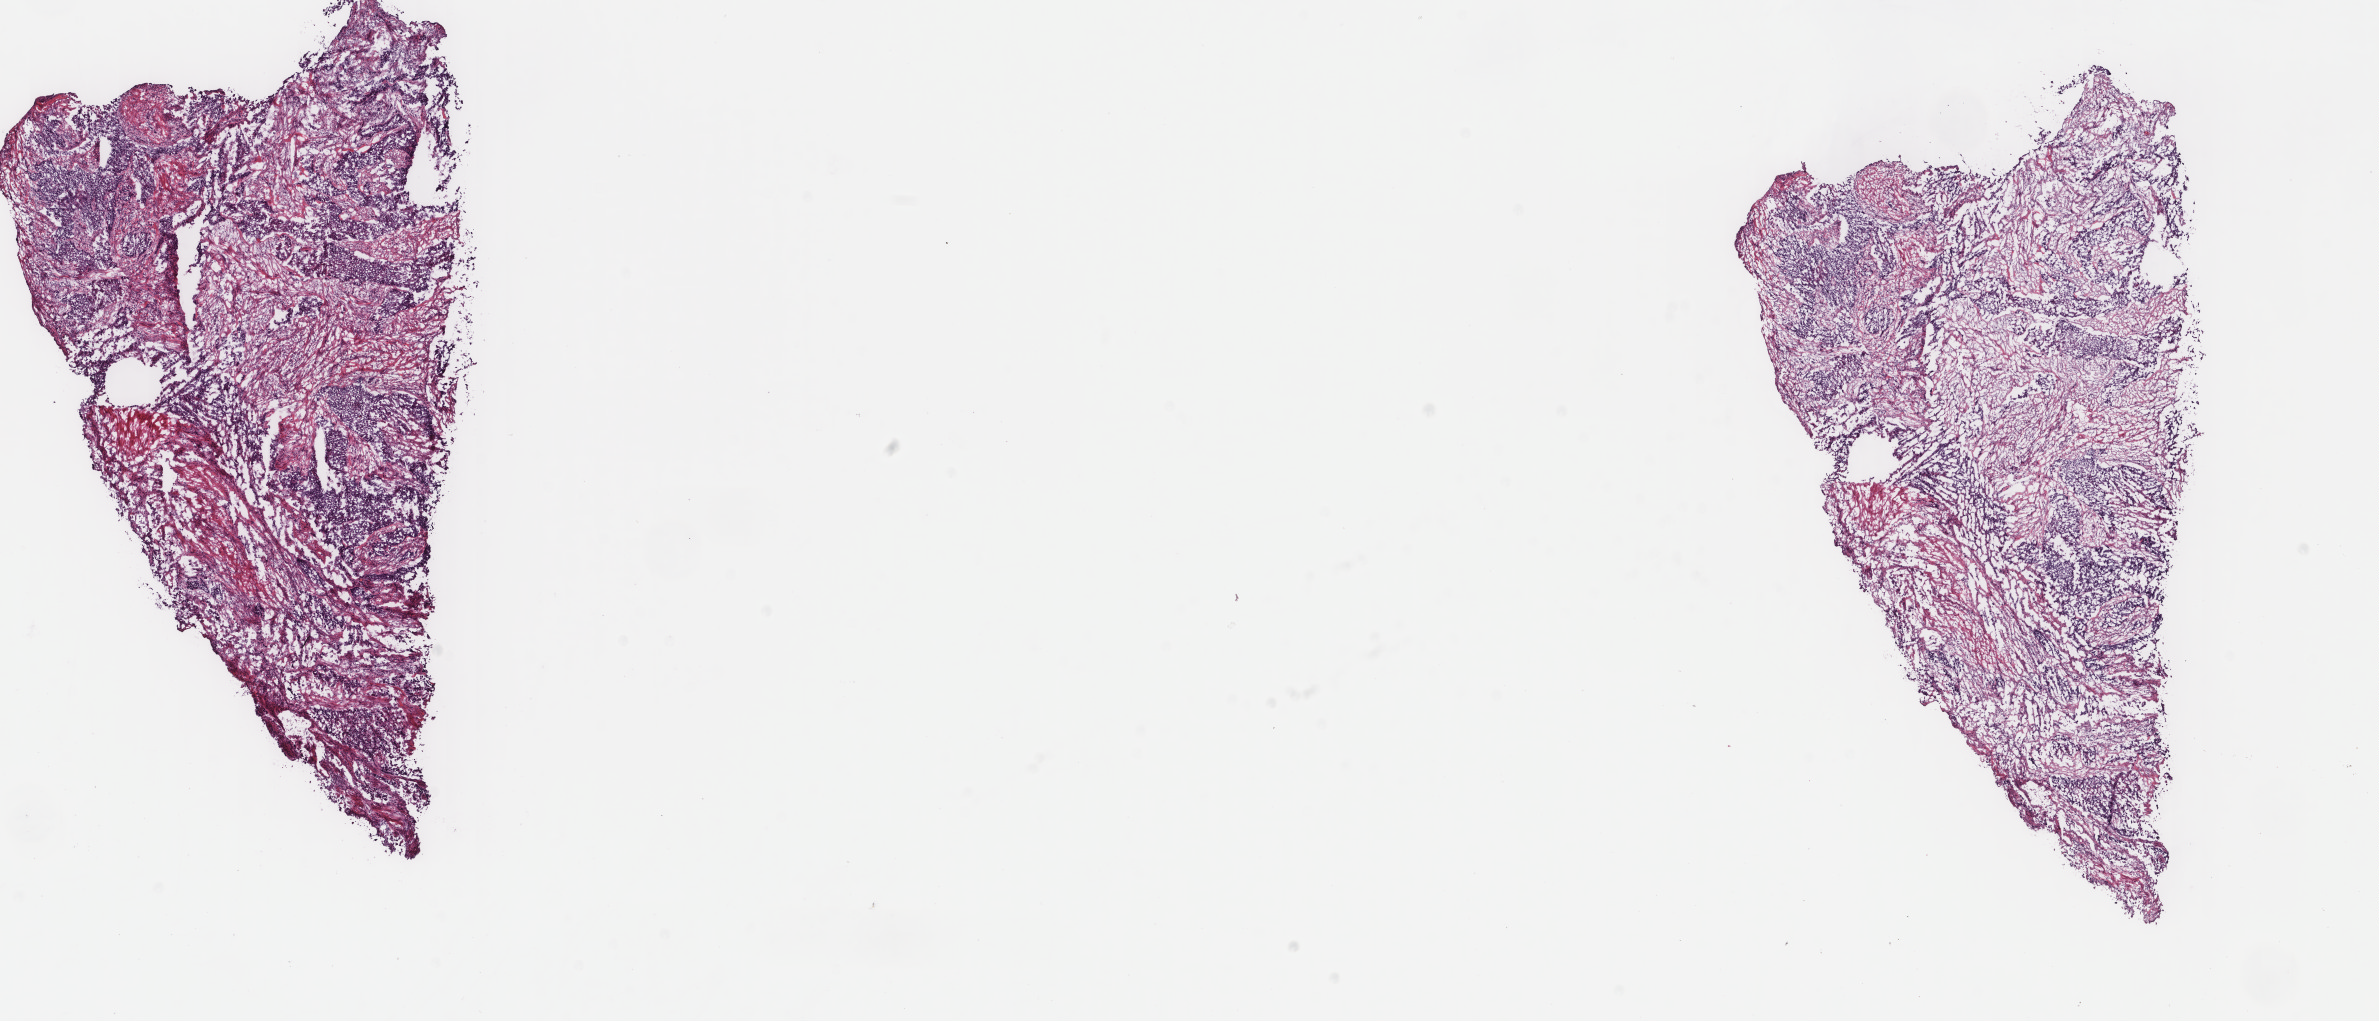
Digitized Hematoxylin and eosin (H&E) stained tissue section (whole slide), low-resolution overview of the scanned area, about 18.9 x 8.1 mm, frozen section from the top of the tissue portion, sample: primary tumour, bladder. Female, age 77 years at initial diagnosis. Histologic grade: high grade. Composition of this section per pathologist review: tumour cells 40%, tumour nuclei 70%, normal cells 0%, stromal cells 55%, necrosis 5%. Inflammatory infiltration, as recorded: lymphocyte infiltration 2%, monocyte infiltration 0%, neutrophil infiltration 0%.
• diagnosis: Transitional cell carcinoma
• AJCC pathologic stage: II (7th edition)